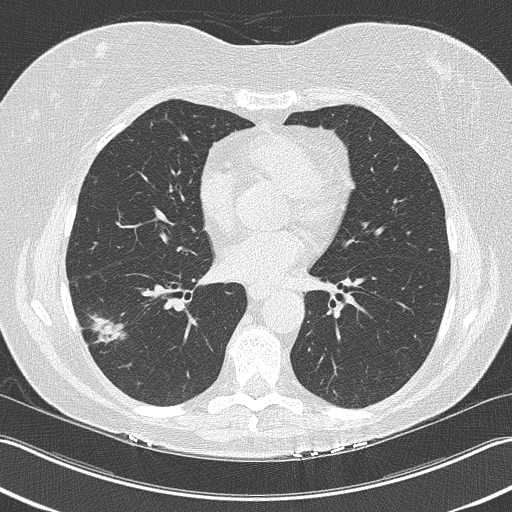
Low-dose screening chest CT, one axial slice. Slice 107 of 210 in the series (ordered by position). Reconstruction kernel B50f. Lung window (W 1500 / L -600 HU). 2 mm slice thickness. 512 × 512 image matrix, field of view 348 × 348 mm.
Structures marked on this image (outlined manually by an expert reader):
- lesion 1 (tumor, lower lobe of right lung): box from (x=84, y=313) to (x=126, y=345) px